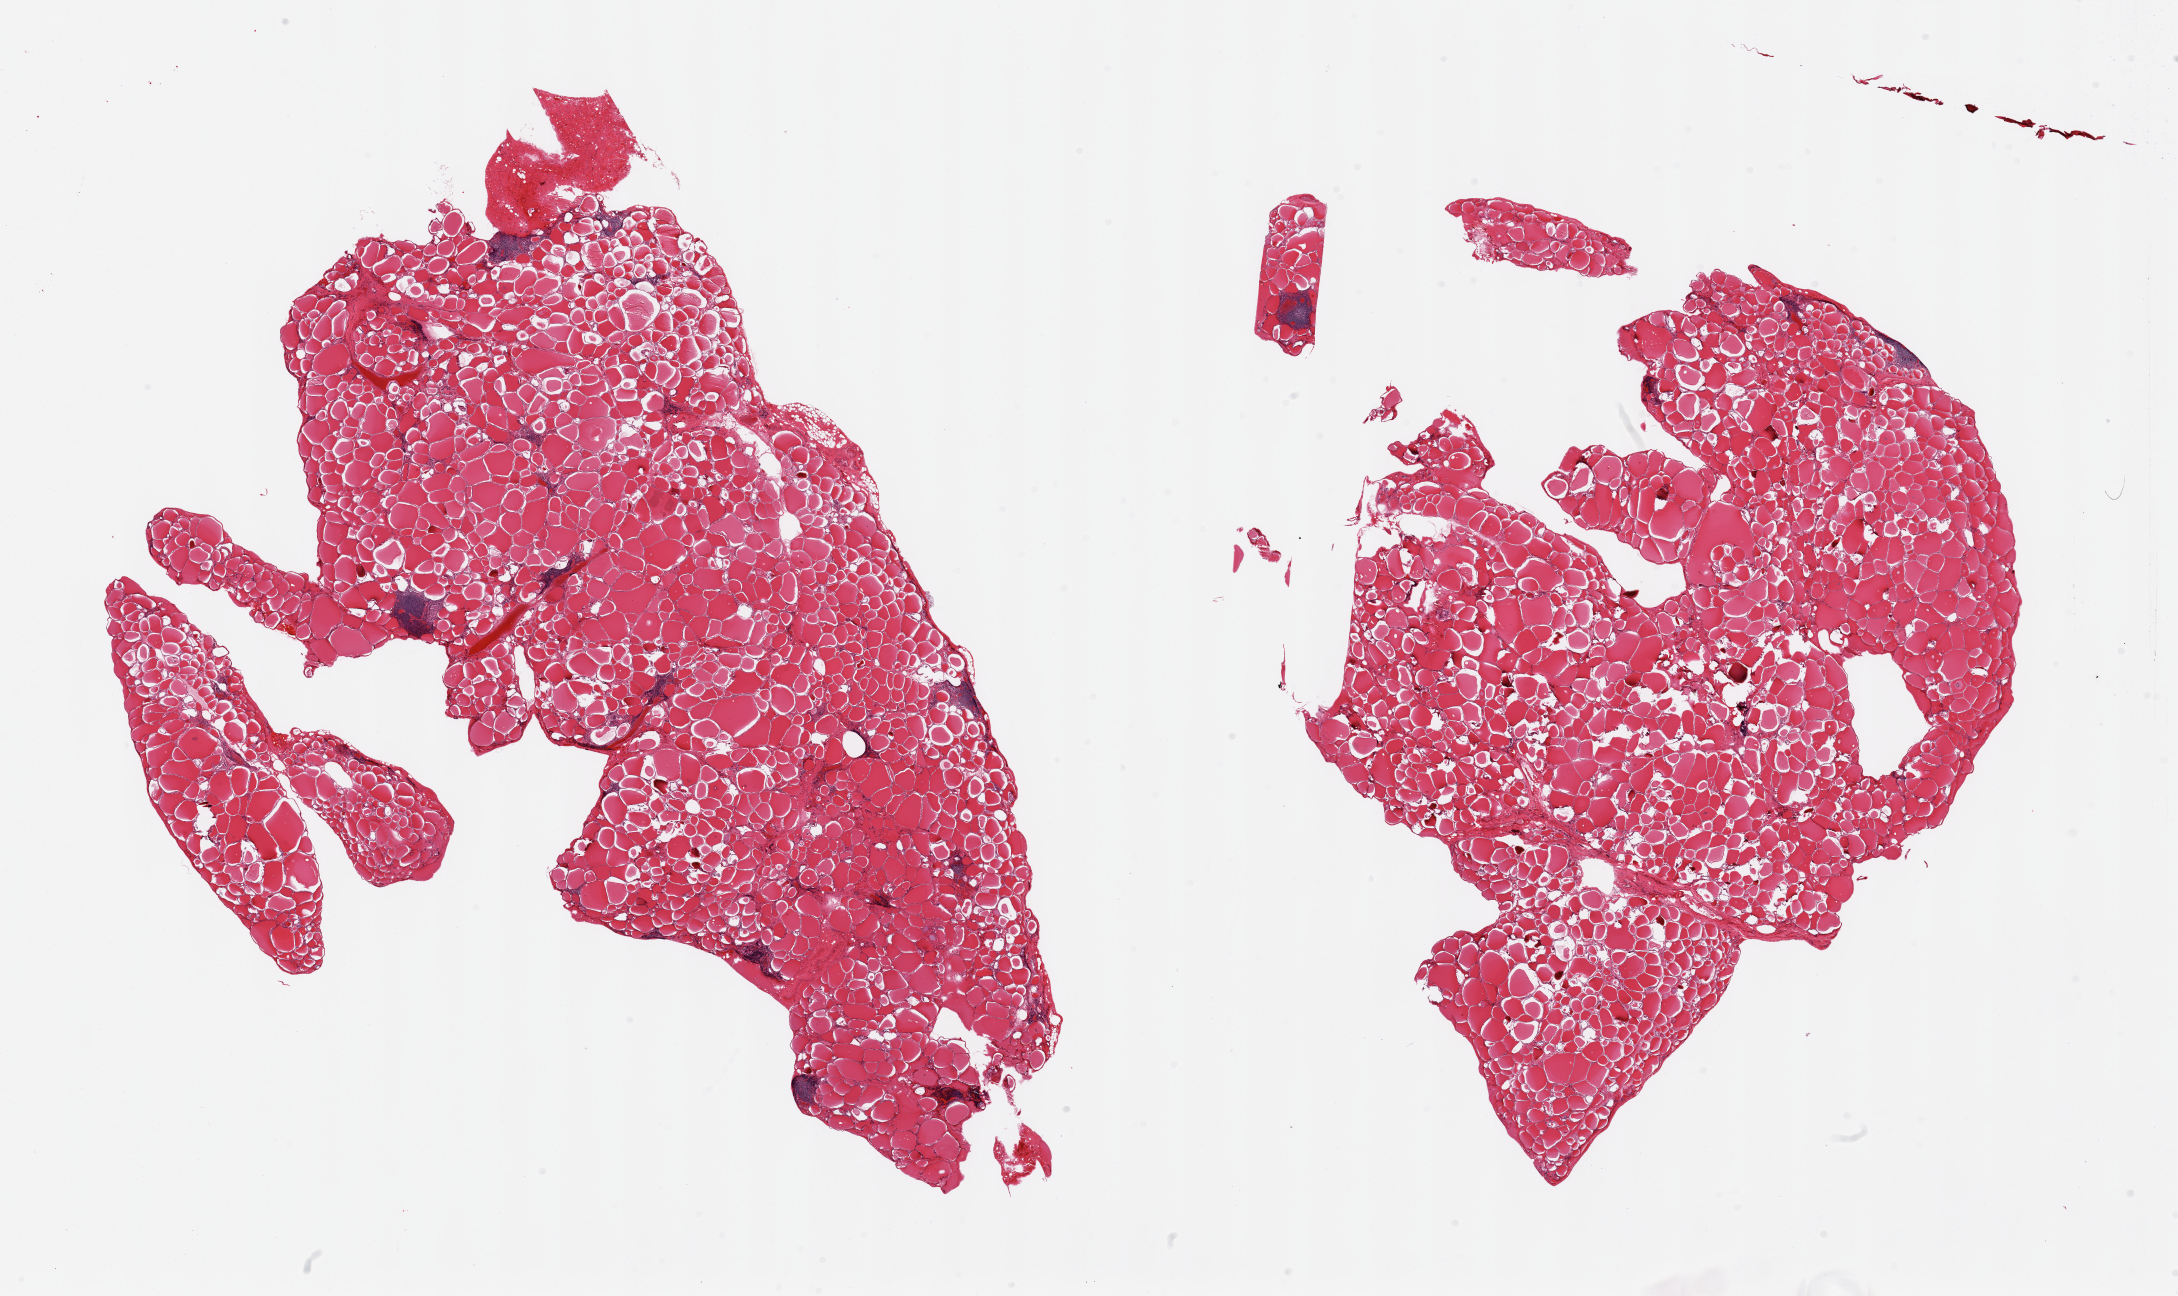
Digitized haematoxylin and eosin-stained section, shown as a low-resolution overview of the whole scanned area (about 34.5 x 20.5 mm); PAXgene-fixed, paraffin-embedded tissue; sampled site (target tissue): thyroid; donor tissue sample. Male donor.
• pathologist's review note for this sample: 2 pieces; occasional lymphoid aggregates